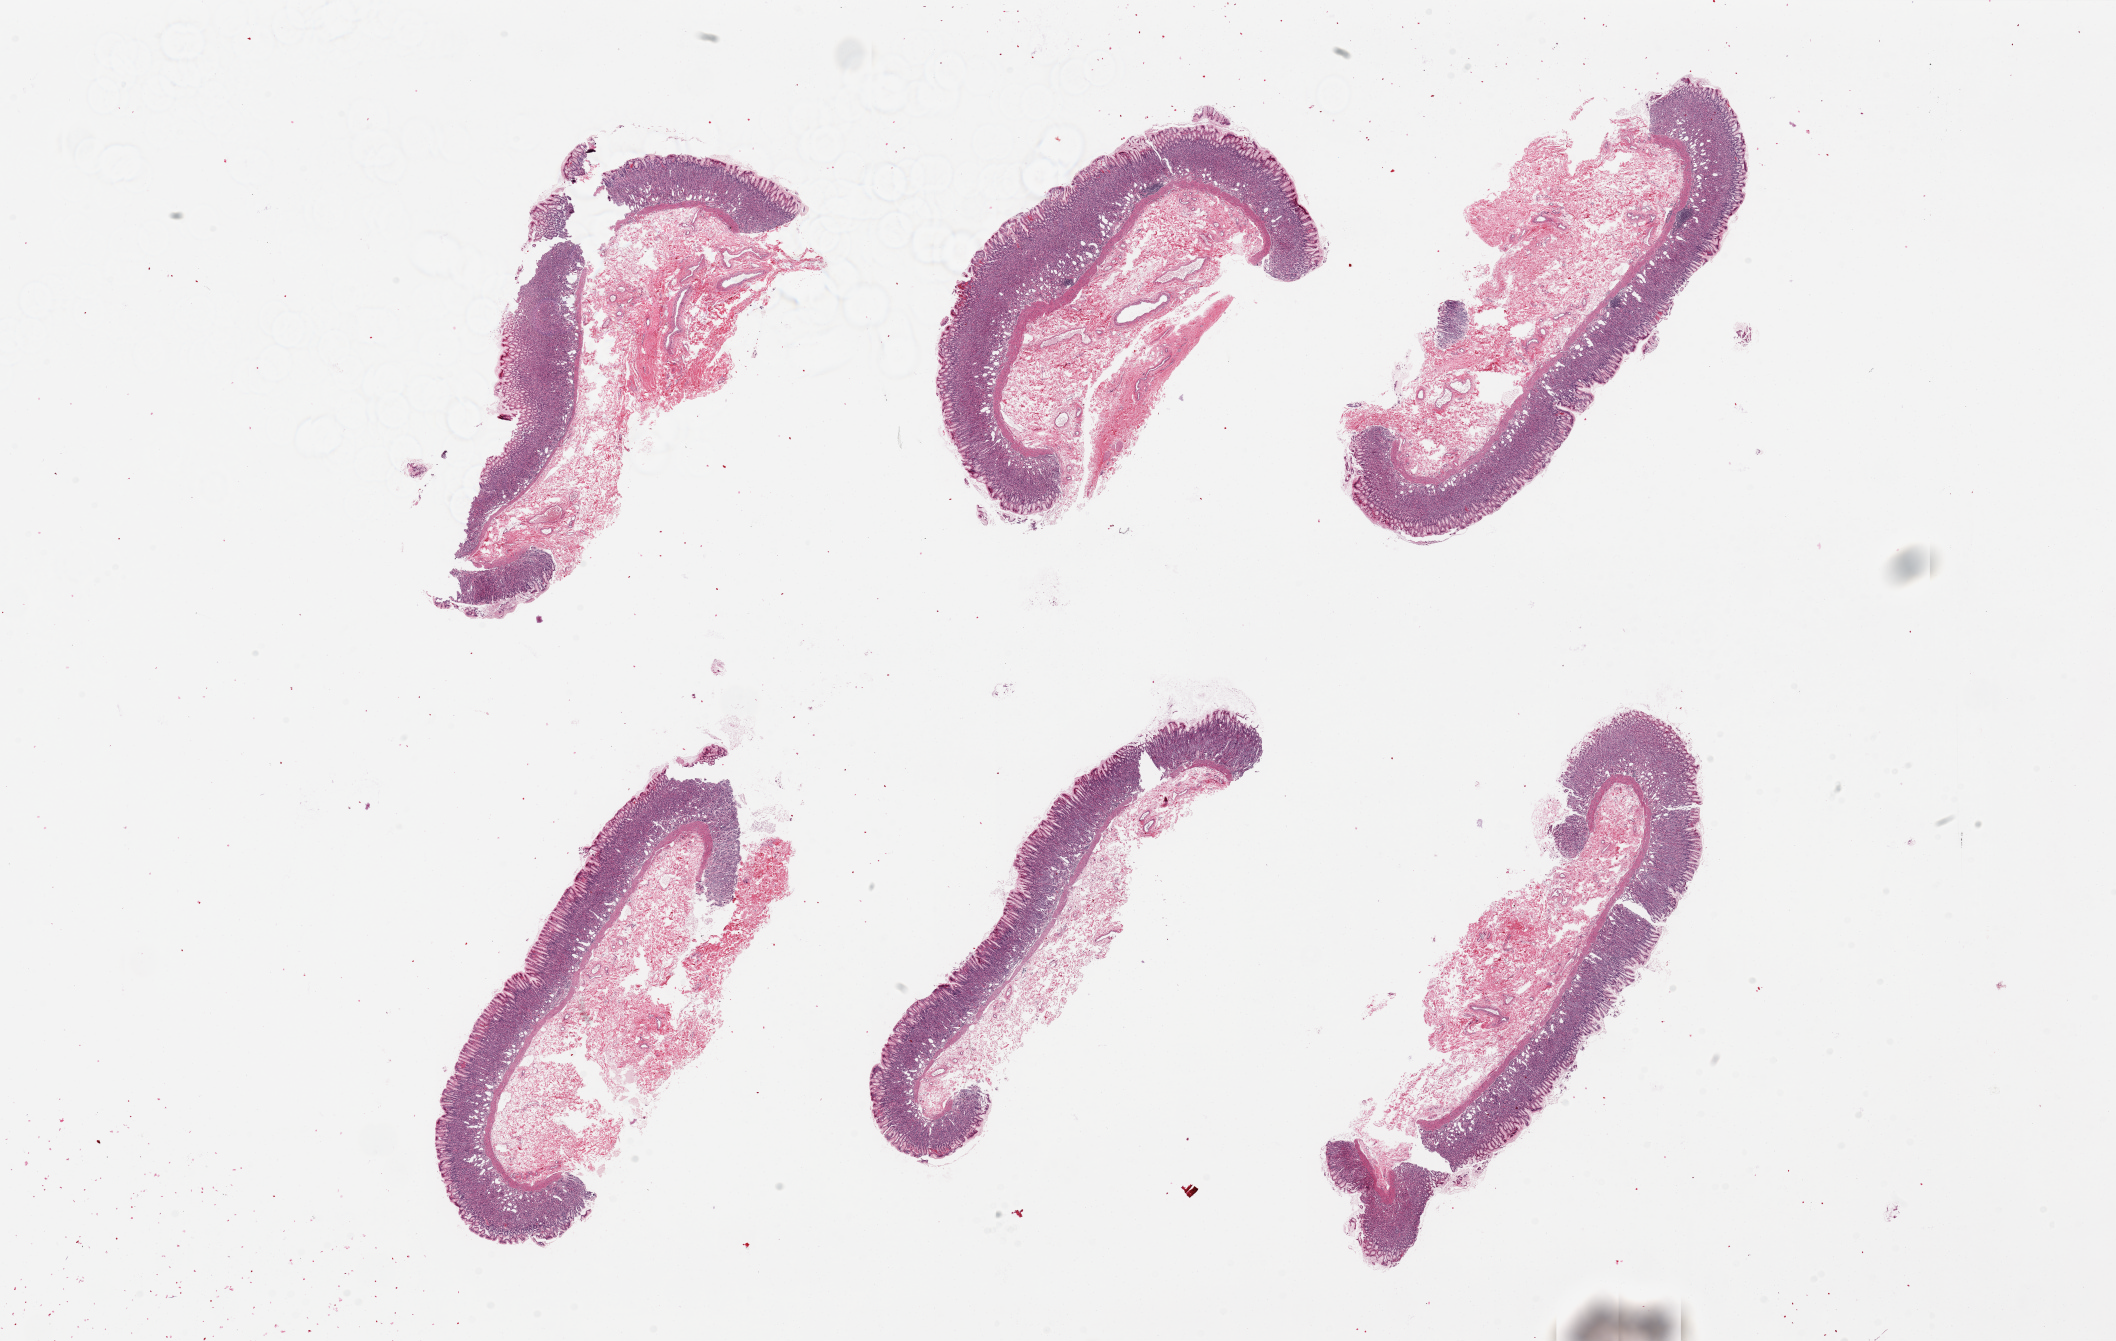
Haematoxylin and eosin whole-slide image, low-resolution overview of the scanned area, about 33.5 x 21.2 mm. PAXgene-fixed, paraffin-embedded tissue. Section of stomach (target tissue). Tissue donor sample. Donor sex: male.
• reviewer comment on this tissue sample: 1 piece. 5x3 mm. Mucosa-submucosa only. Basilar gland dilatation